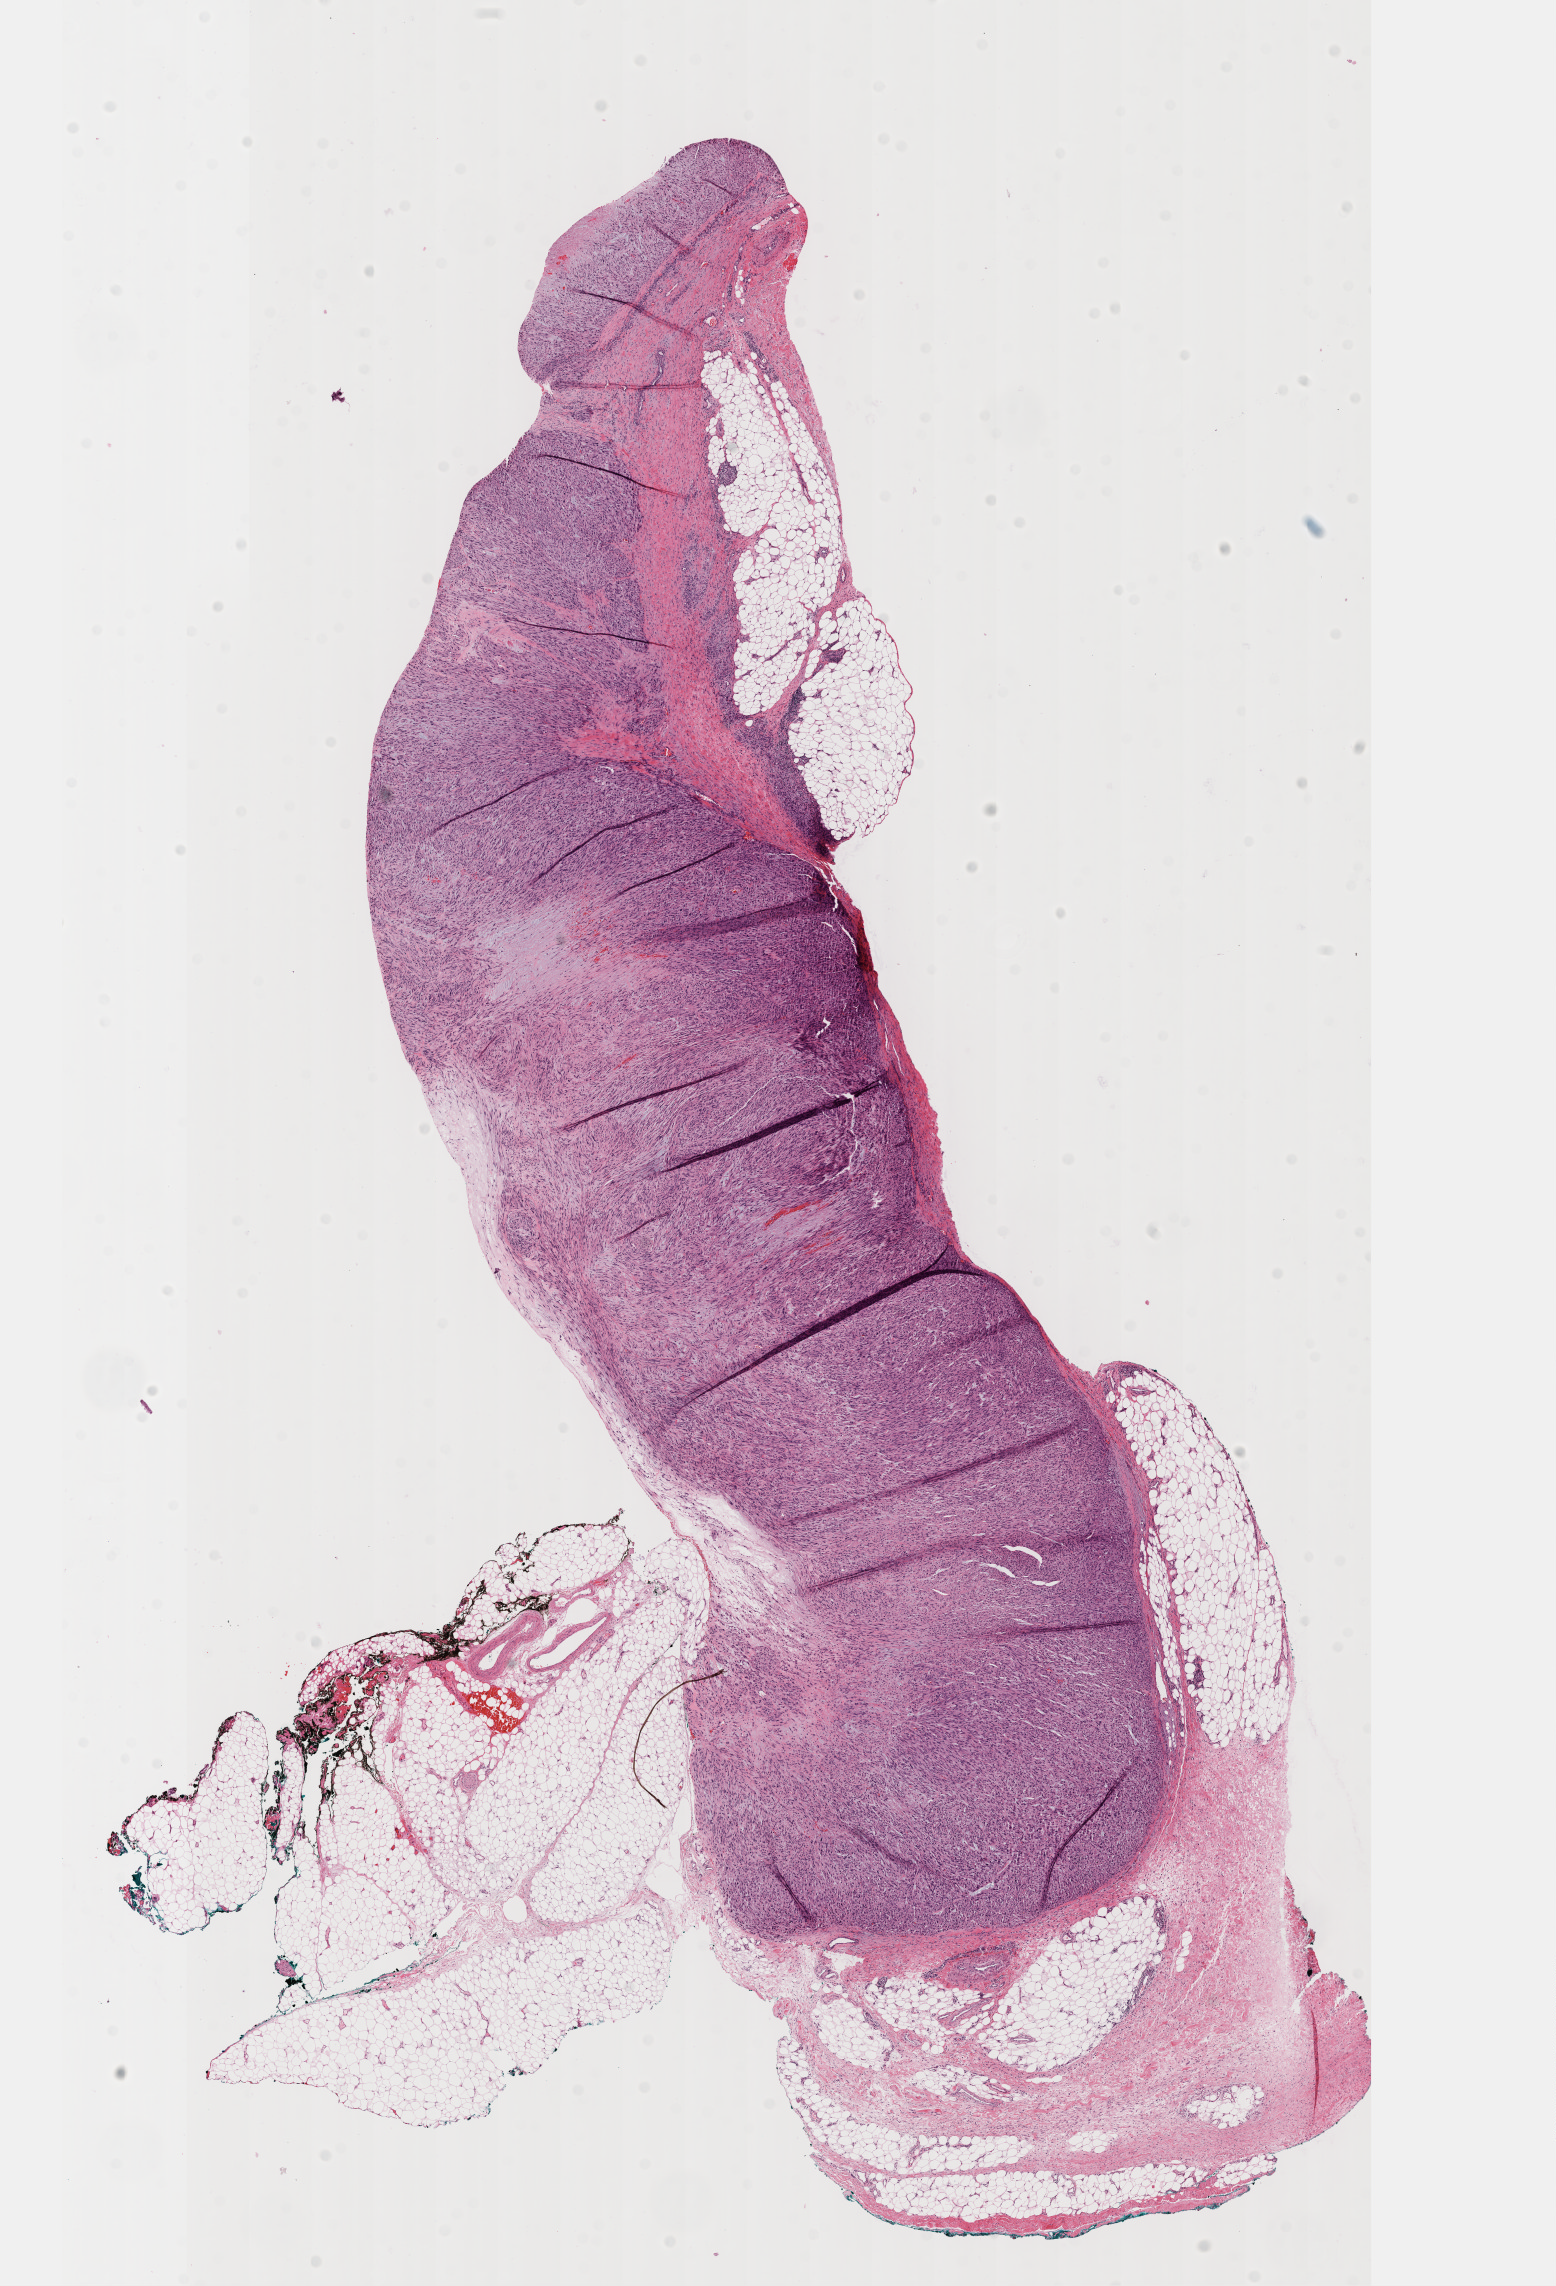
H&E-stained whole-slide image — a low-resolution overview of the entire scanned area, about 12.6 x 18.5 mm (from a 40x scan); FFPE section; primary tumour sample from the connective, subcutaneous and other soft tissues. Patient: female, age at initial diagnosis 63 years.
Histologic diagnosis: Leiomyosarcoma, NOS (connective, subcutaneous and other soft tissues of lower limb and hip).